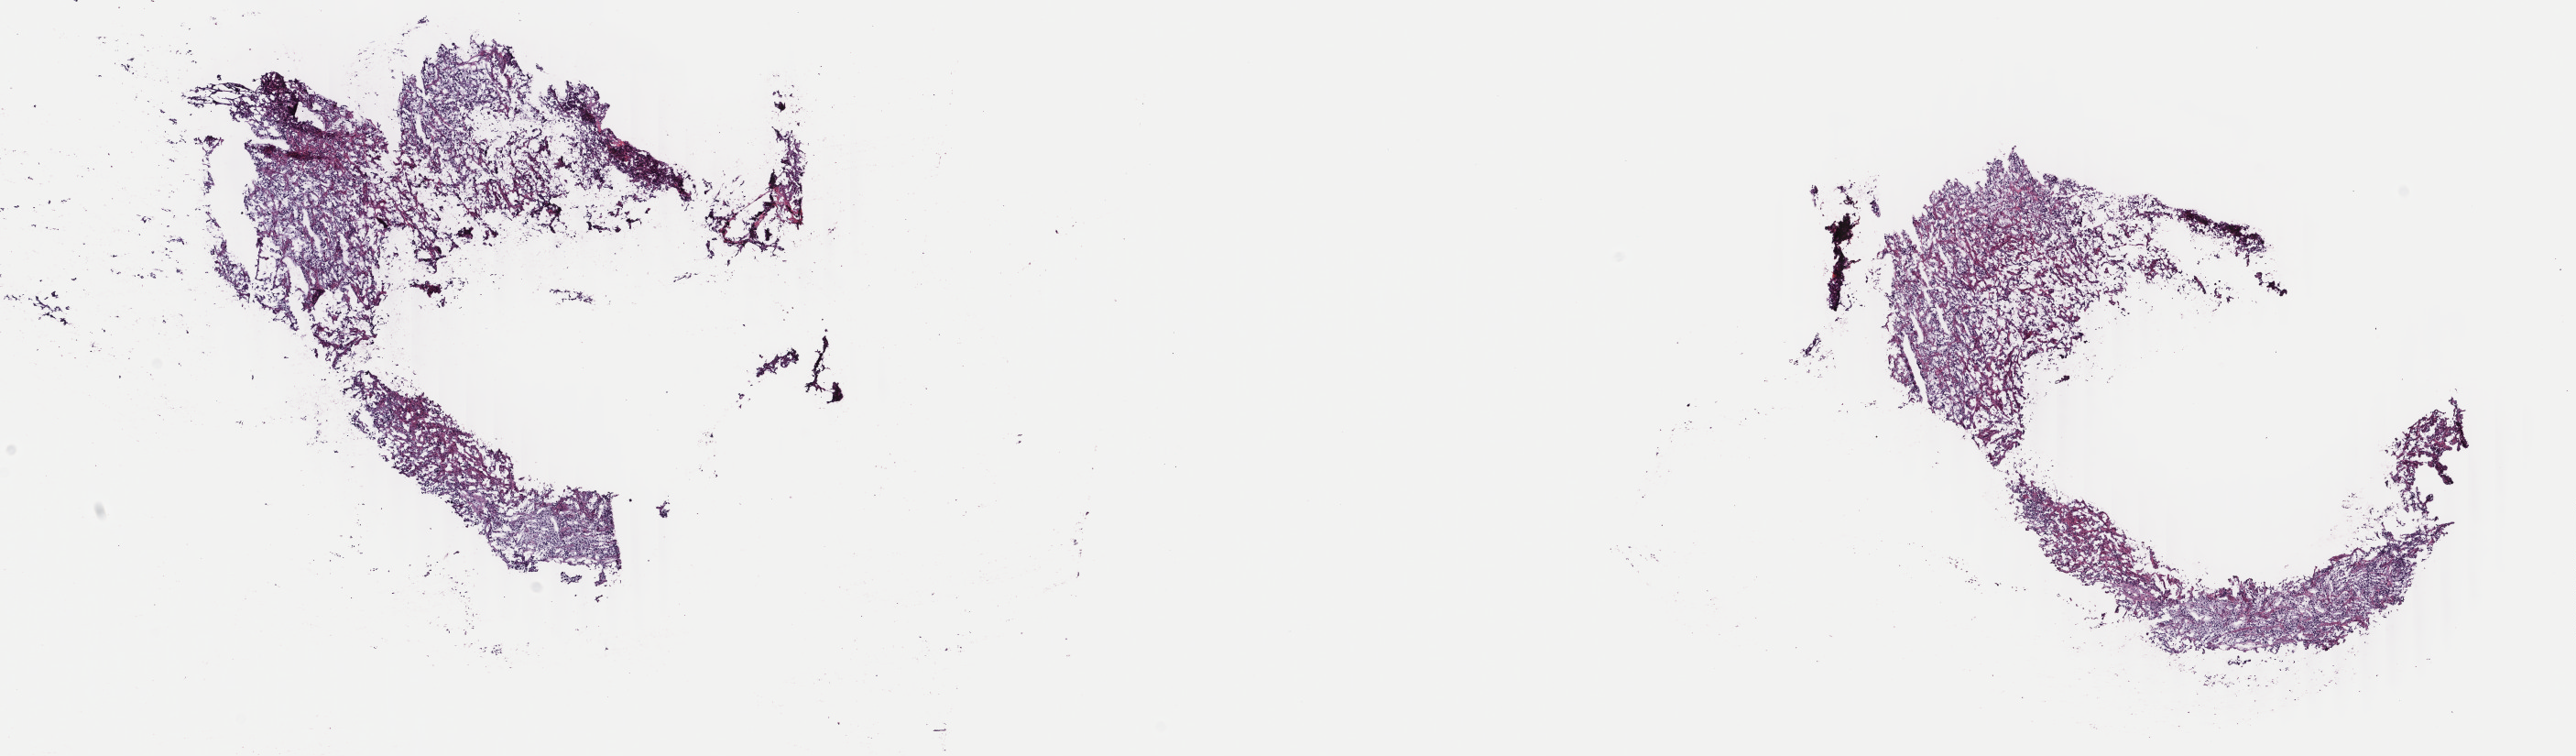
Whole-slide histology image, H&E — shown as a low-resolution overview of the whole scanned area (about 22.4 x 6.6 mm, from a 40x scan), frozen section, primary tumour sample from the connective, subcutaneous and other soft tissues. Male, age 61 years at initial diagnosis. Composition of this section per pathologist review: tumour cells 100%, tumour nuclei 80%, normal cells 0%, stromal cells 0%, necrosis 0%. Infiltration values recorded for this section: lymphocyte infiltration 1%, monocyte infiltration 0%, neutrophil infiltration 0%.
- lymph nodes positive (case pathology): 0 of 1 examined
- histologic diagnosis: Extra-adrenal paraganglioma, NOS